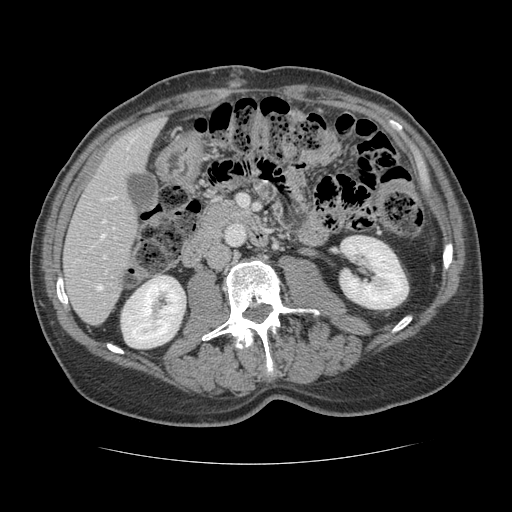
Contrast-enhanced abdominal CT, one axial slice. Slice 48 of 134 in the series (ordered by position). Reconstruction kernel STANDARD. 120 kVp. Intravenous contrast given. Soft-tissue window (W 400 / L 40 HU). 2.5 mm slice thickness. 512 × 512 image matrix, field of view 377 × 377 mm. Male patient, age 68 years. From the clinical record (not read from this slice): diagnosis: colorectal cancer liver metastases, imaged before liver resection; multiple liver metastases: yes; largest metastasis: 2.2 cm.
Outlined on this slice (outlined manually by an expert reader):
- hepatic veins: bounding box <101,148,128,238> (left, top, right, bottom; pixels)
- liver: <65,118,164,325>
- planned liver remnant (the part of the liver to remain after resection): <65,118,163,325>
- portal vein (with intrahepatic branches): <97,256,106,290>